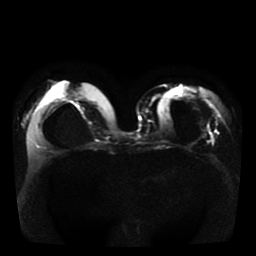
Breast MRI, one axial slice; position 15 of 41 along the scan axis; diffusion-weighted series; image 2 of 4 stored at this slice position (different b-values; order by instance number); 1.5 T; 5 mm slice thickness; 256 × 256 image matrix, field of view 330 × 330 mm. Female patient.
Annotated regions visible in this slice (outlined manually by an expert reader):
- tumour on diffusion-weighted imaging: bounding box <202,135,206,138> (left, top, right, bottom; pixels)